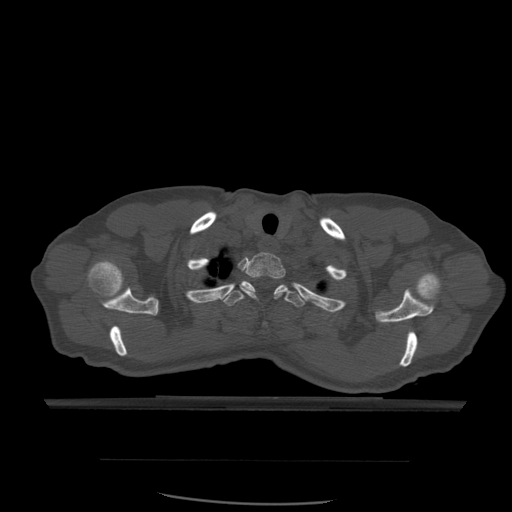
CT including the spine, one axial slice; position 464 of 574 along the scan axis; bone window (W 1800 / L 400 HU); 1.25 mm slice thickness; 512 × 512 image matrix, field of view 392 × 392 mm. Patient age 48 years. From the clinical record (not read from this slice): primary cancer: lung.
Structures marked on this image (semi-automatically segmented with operator editing):
- T1 vertebra: bounding box (x1, y1, x2, y2) in pixels: (241, 252, 286, 300)
- T2 vertebra: (223, 281, 306, 307)